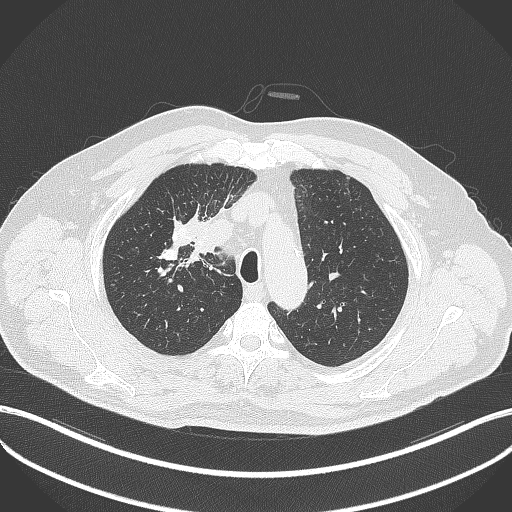
Chest CT, one axial slice. Slice 305 of 411 in the series (ordered by position). Reconstruction kernel B70f. 120 kVp. Lung window (W 1500 / L -600 HU). 1 mm slice thickness. 512 × 512 image matrix, field of view 400 × 400 mm. Male patient, age 60 years. From the clinical record (not read from this slice): clinical TNM (as recorded): T1b N1 M0.
Structures marked on this image (bounding box drawn by a radiologist):
- lung tumour (recorded histology: squamous cell carcinoma): bounding box <189,228,217,262> (left, top, right, bottom; pixels)